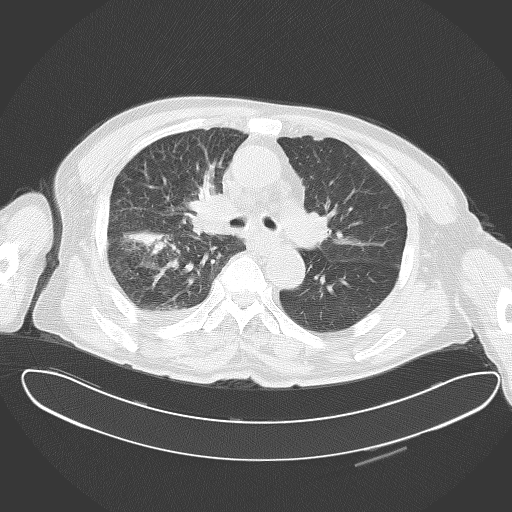
Chest CT, one axial slice. Slice 37 of 62 in the series (ordered by position). Reconstruction kernel B70f. Lung window (W 1500 / L -600 HU). 5 mm slice thickness. 512 × 512 image matrix, field of view 427 × 427 mm. Male patient, age 78 years. From the clinical record (not read from this slice): clinical TNM (as recorded): T2 N1 M1.
Outlined on this slice (bounding box drawn by a radiologist):
- lung tumour (recorded histology: adenocarcinoma): bounding box [x1, y1, x2, y2] px = [125, 177, 227, 267]